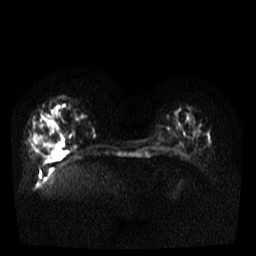
Breast MRI, one axial slice. Position 10 of 34 along the scan axis. Diffusion-weighted series; image 2 of 4 stored at this slice position (different b-values; order by instance number). 3 T. 5 mm slice thickness. 256 × 256 image matrix. Female patient.
Annotated regions visible in this slice (manually delineated by an expert):
- tumour on diffusion-weighted imaging: bounding box <39,135,57,155> (left, top, right, bottom; pixels)